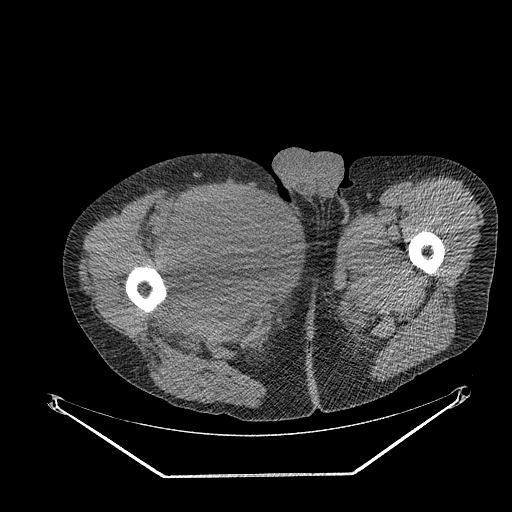
CT of an extremity soft-tissue mass (from a PET/CT study), one axial slice. Slice 280 of 311 in the series (ordered by position). Reconstruction kernel STANDARD. 140 kVp. Soft-tissue window (W 400 / L 40 HU). 3.75 mm slice thickness. 512 × 512 image matrix, field of view 500 × 500 mm. Male patient. From the clinical record (not read from this slice): histological type: undifferentiated - pleiomorphic; grade: high; site of the primary tumour: right thigh.
Annotated regions visible in this slice (expert contour drawn on MRI and transferred to this co-registered scan by the dataset authors):
- gross tumour volume including surrounding oedema: bounding box <176,190,261,277> (left, top, right, bottom; pixels)
- gross tumour volume (mass): <174,192,259,277>